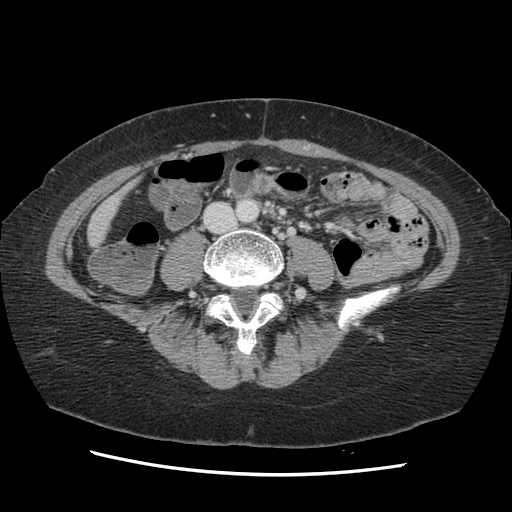
Contrast-enhanced abdominal CT, one axial slice; slice 15 of 141 in the series (ordered by position); 120 kVp; soft-tissue window (W 400 / L 40 HU); 512 × 512 image matrix. Female patient, age 61 years. Case-level facts recorded for this patient, not image findings: diagnosis: colorectal cancer liver metastases, imaged before liver resection; multiple liver metastases: no; largest metastasis: 2.4 cm; disease in both lobes: no.
Structures marked on this image (manually delineated by an expert):
- liver: bounding box [x1, y1, x2, y2] px = [89, 187, 129, 246]
- planned liver remnant (the part of the liver to remain after resection): [89, 185, 131, 246]